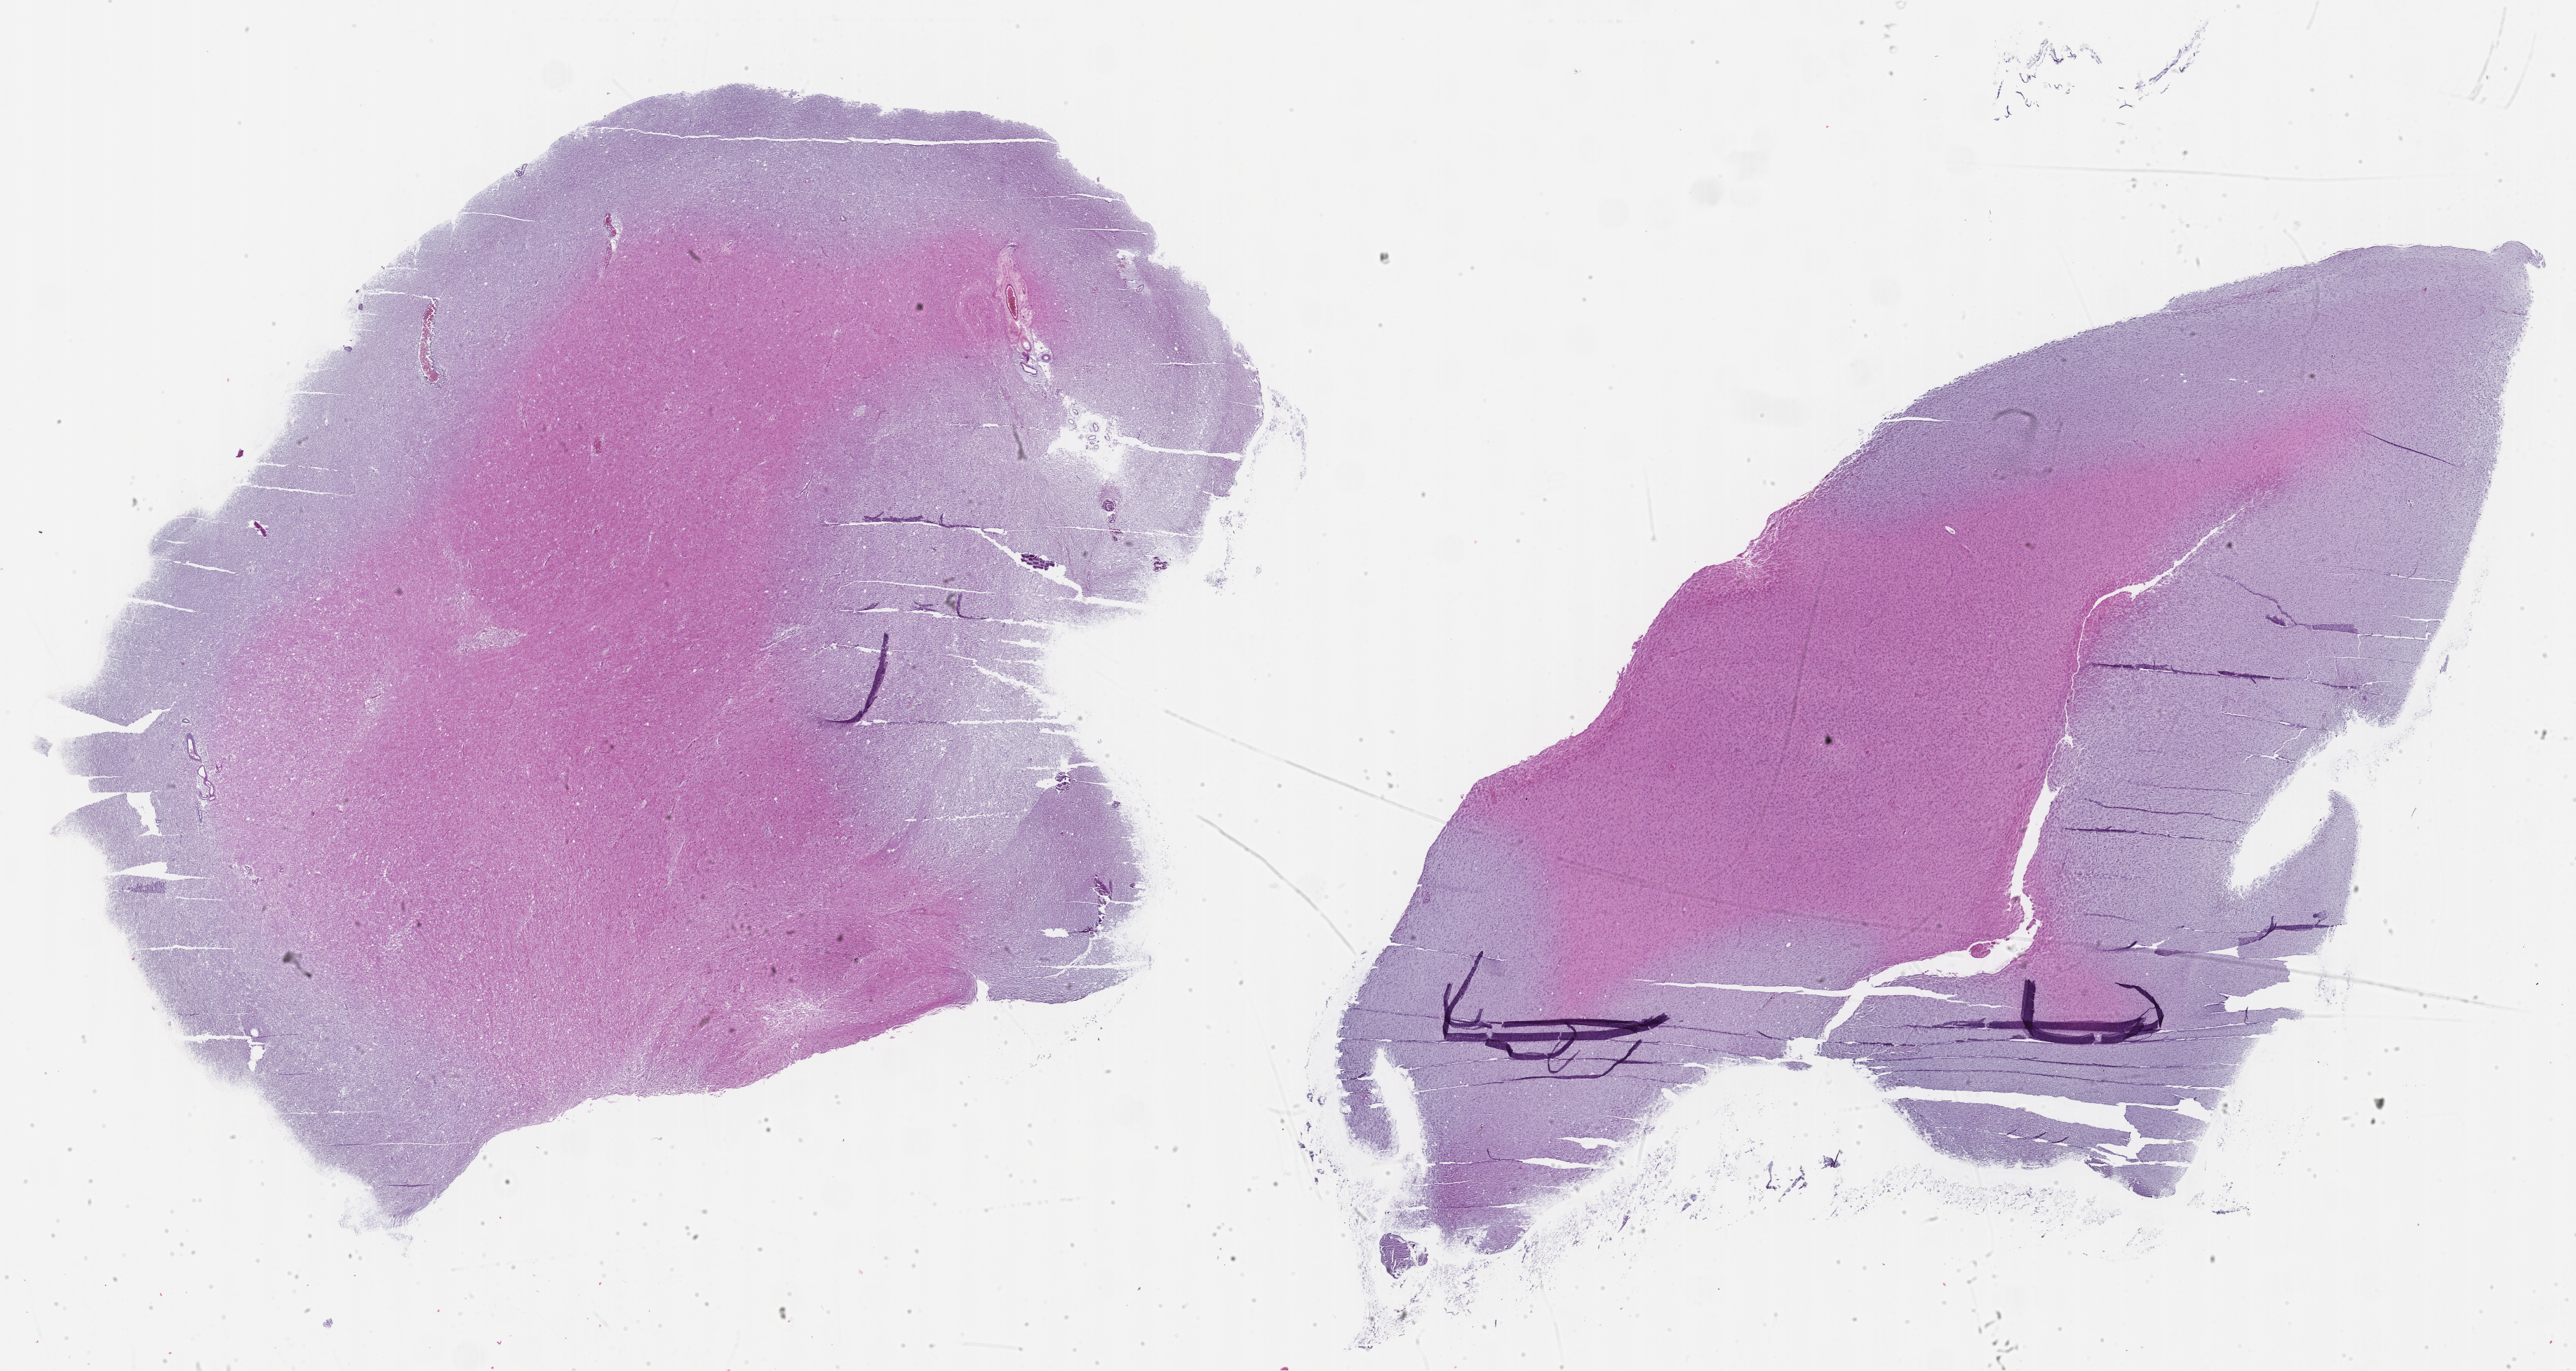
Hematoxylin and eosin (H&E) stained whole-slide image, whole scanned area (about 29.8 x 15.8 mm) shown as a low-resolution overview. Formalin-fixed paraffin-embedded (FFPE) diagnostic section. Brain, primary tumour sample. Male patient; age at initial diagnosis 61 years.
Pathologic diagnosis: Glioblastoma.